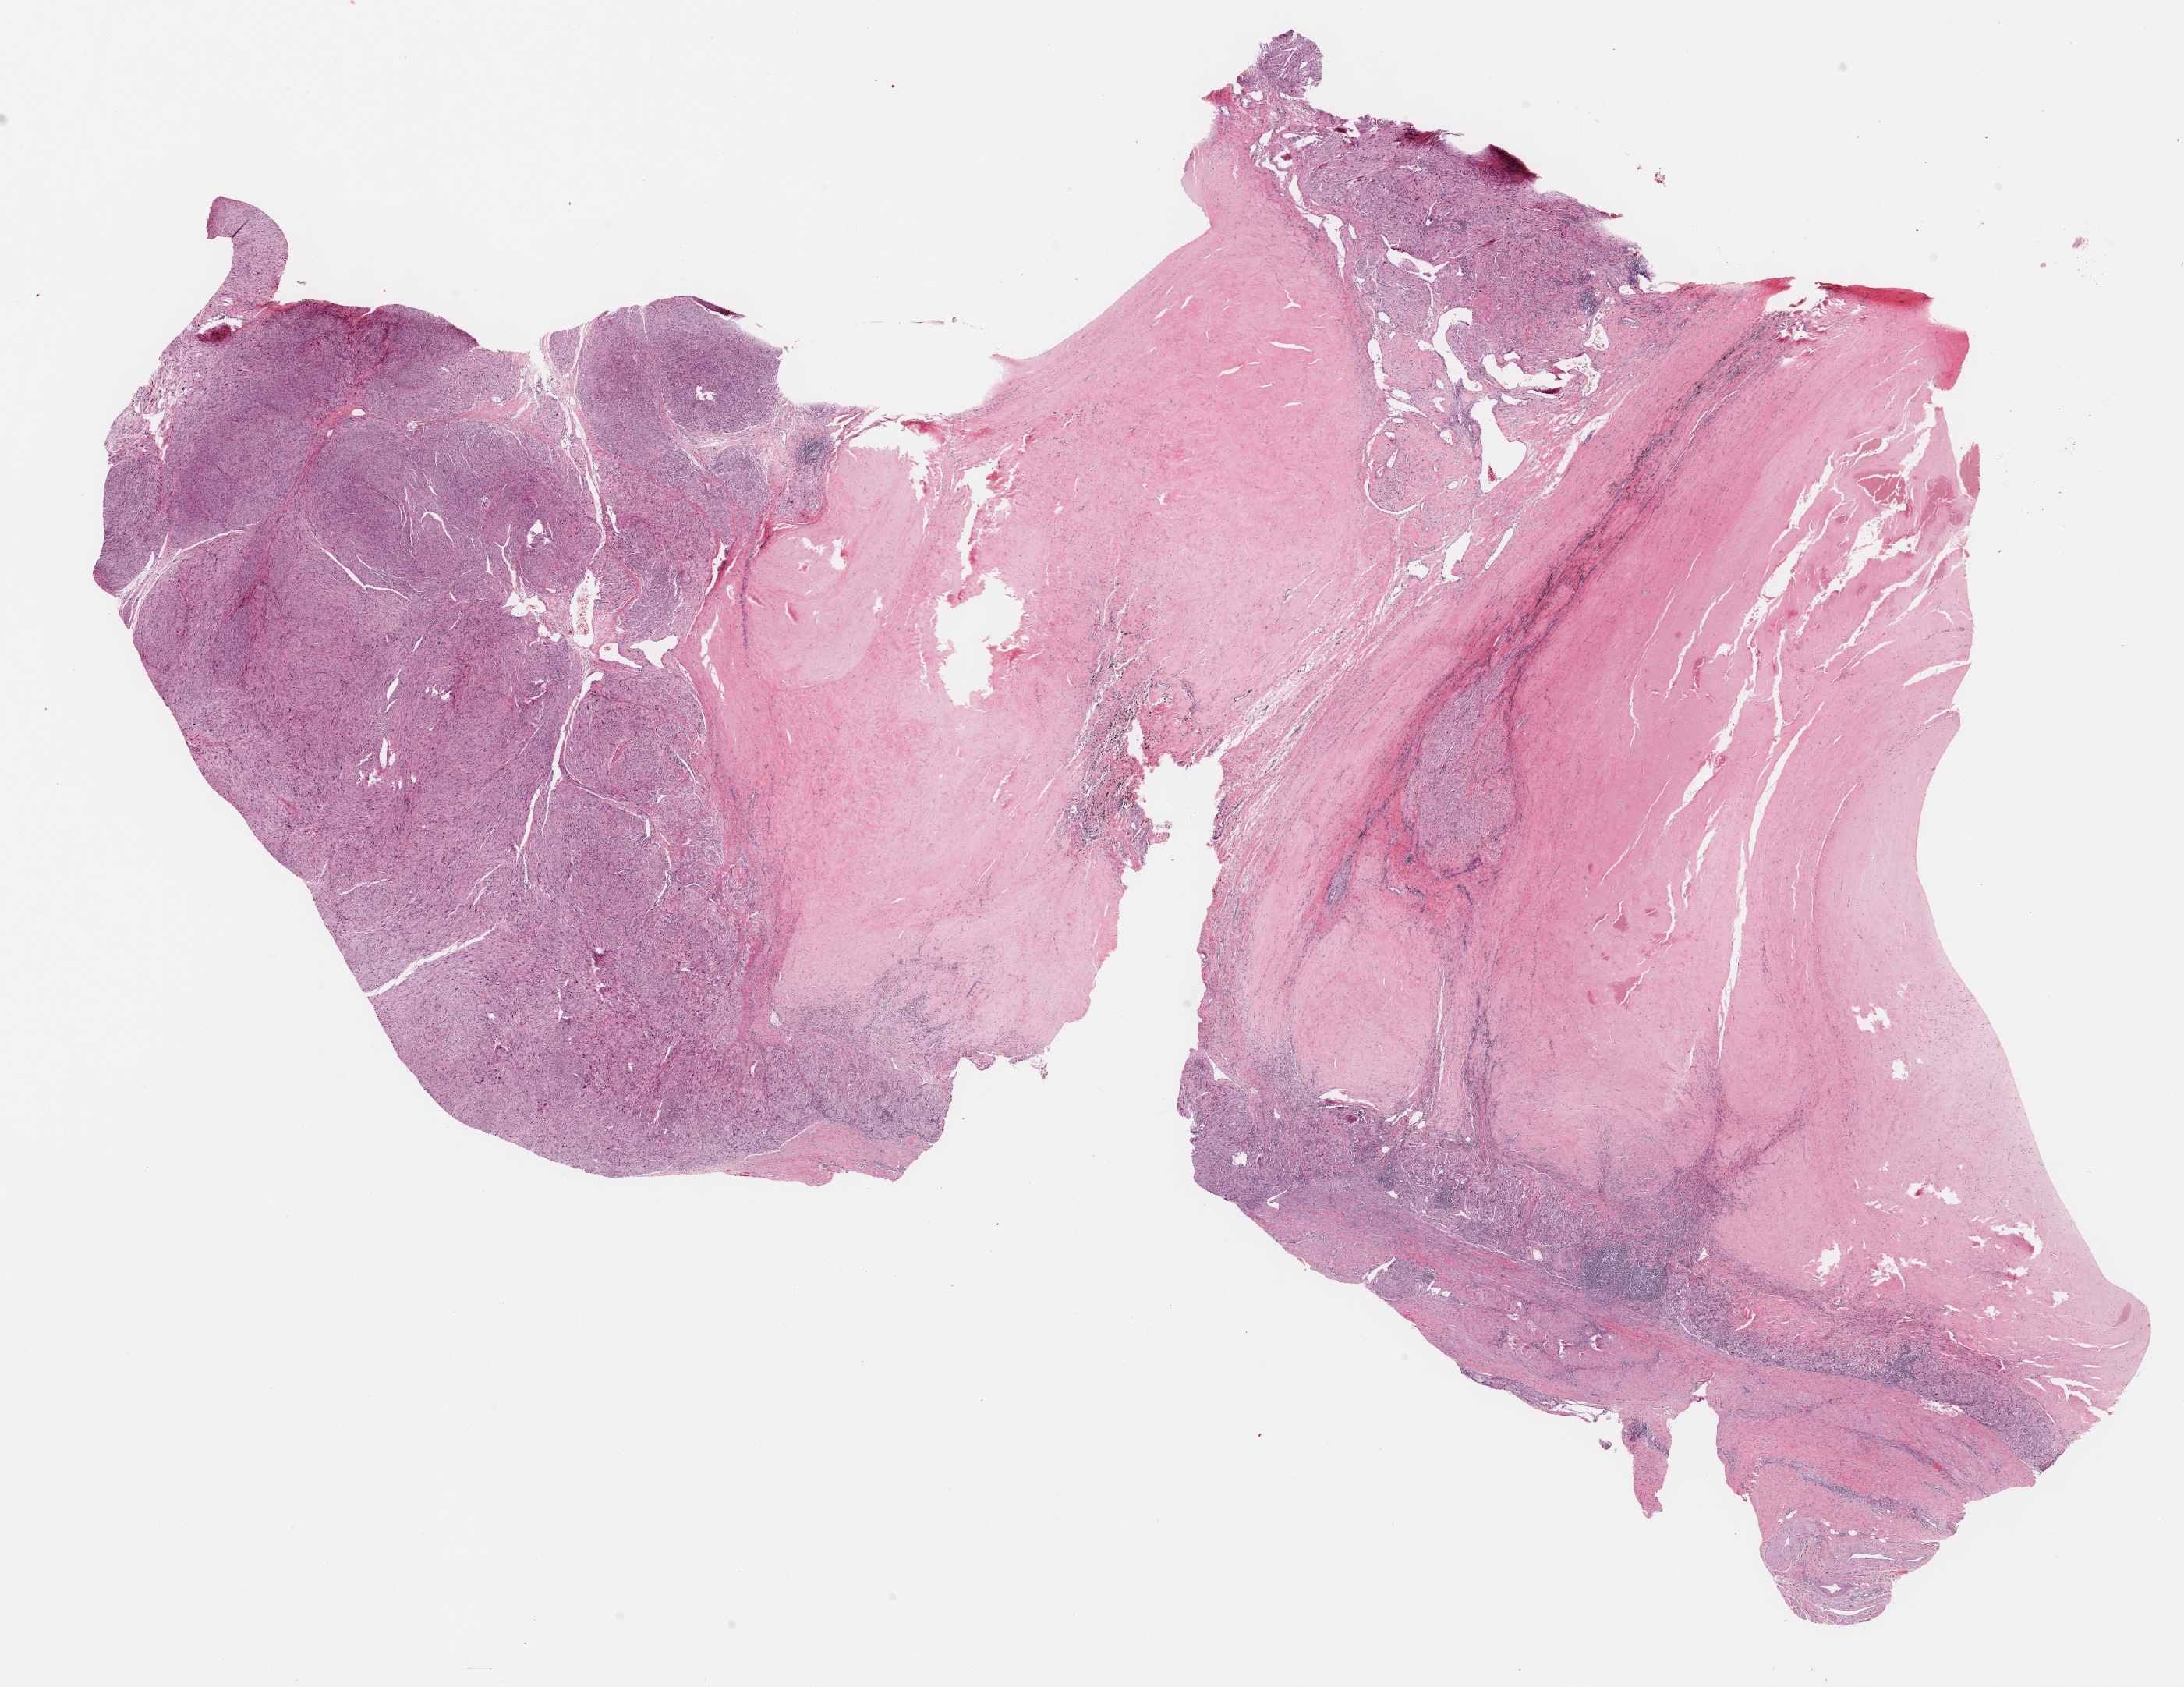
Whole-slide histology image, H&E — shown as a low-resolution overview of the whole scanned area (about 22.7 x 17.5 mm), formalin-fixed paraffin-embedded (FFPE) diagnostic section, primary tumour sample from the retroperitoneum and peritoneum. Patient sex: female.
Histologic diagnosis: Leiomyosarcoma, NOS (retroperitoneum).